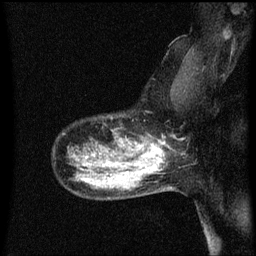
Breast MRI (dynamic contrast-enhanced), one sagittal slice; position 47 of 60 along the scan axis; dynamic contrast-enhanced series, image 2 of 3 at this slice position (ordered by acquisition); 1.5 T; TE 4.2 ms, TR 8.4 ms; 2 mm slice thickness; 256 × 256 image matrix, field of view 200 × 200 mm. Patient: female, 50 years.
Outlined on this slice (semi-automatically segmented with operator editing):
- analysis volume of interest (the breast-tissue region the enhancement analysis was run in; not a lesion): bounding box (x1, y1, x2, y2) in pixels: (100, 128, 153, 171)
- tumour enhancement mask (voxels above the 70 % enhancement threshold inside the analysis volume of interest): (116, 140, 153, 171)